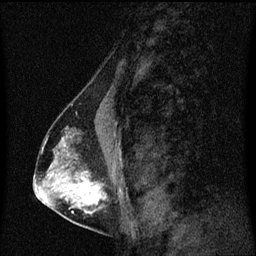
Breast MRI (dynamic contrast-enhanced), one sagittal slice. Position 35 of 60 along the scan axis. Dynamic contrast-enhanced series, image 2 of 3 at this slice position (ordered by acquisition). 1.5 T. TE 4.2 ms, TR 8.4 ms. 2 mm slice thickness. 256 × 256 image matrix, field of view 200 × 200 mm. Female patient, age 40 years. Case-level facts recorded for this patient, not image findings: setting: breast cancer imaged before/during neoadjuvant chemotherapy; receptor status: triple-negative.
Outlined on this slice (semi-automatic segmentation, software-assisted and operator-edited):
- analysis volume of interest (the breast-tissue region the enhancement analysis was run in; not a lesion): box from (x=44, y=128) to (x=119, y=221) px
- tumour enhancement mask (voxels above the 70 % enhancement threshold inside the analysis volume of interest): (x=63, y=146)–(x=106, y=207)